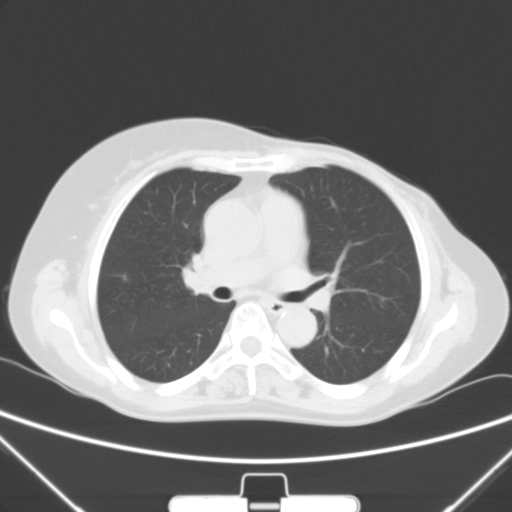
Chest CT, one axial slice; position 30 of 53 along the scan axis; 120 kVp; lung window (W 1500 / L -600 HU); 512 × 512 image matrix, field of view 350 × 350 mm. Patient: female, 64 years. Case-level facts recorded for this patient, not image findings: clinical TNM (as recorded): T1c N0 M0; histopathological grade: G1-2.
Outlined on this slice (rectangle marked by the reading radiologist):
- lung tumour (recorded histology: adenocarcinoma): bounding box [x1, y1, x2, y2] px = [114, 271, 132, 291]